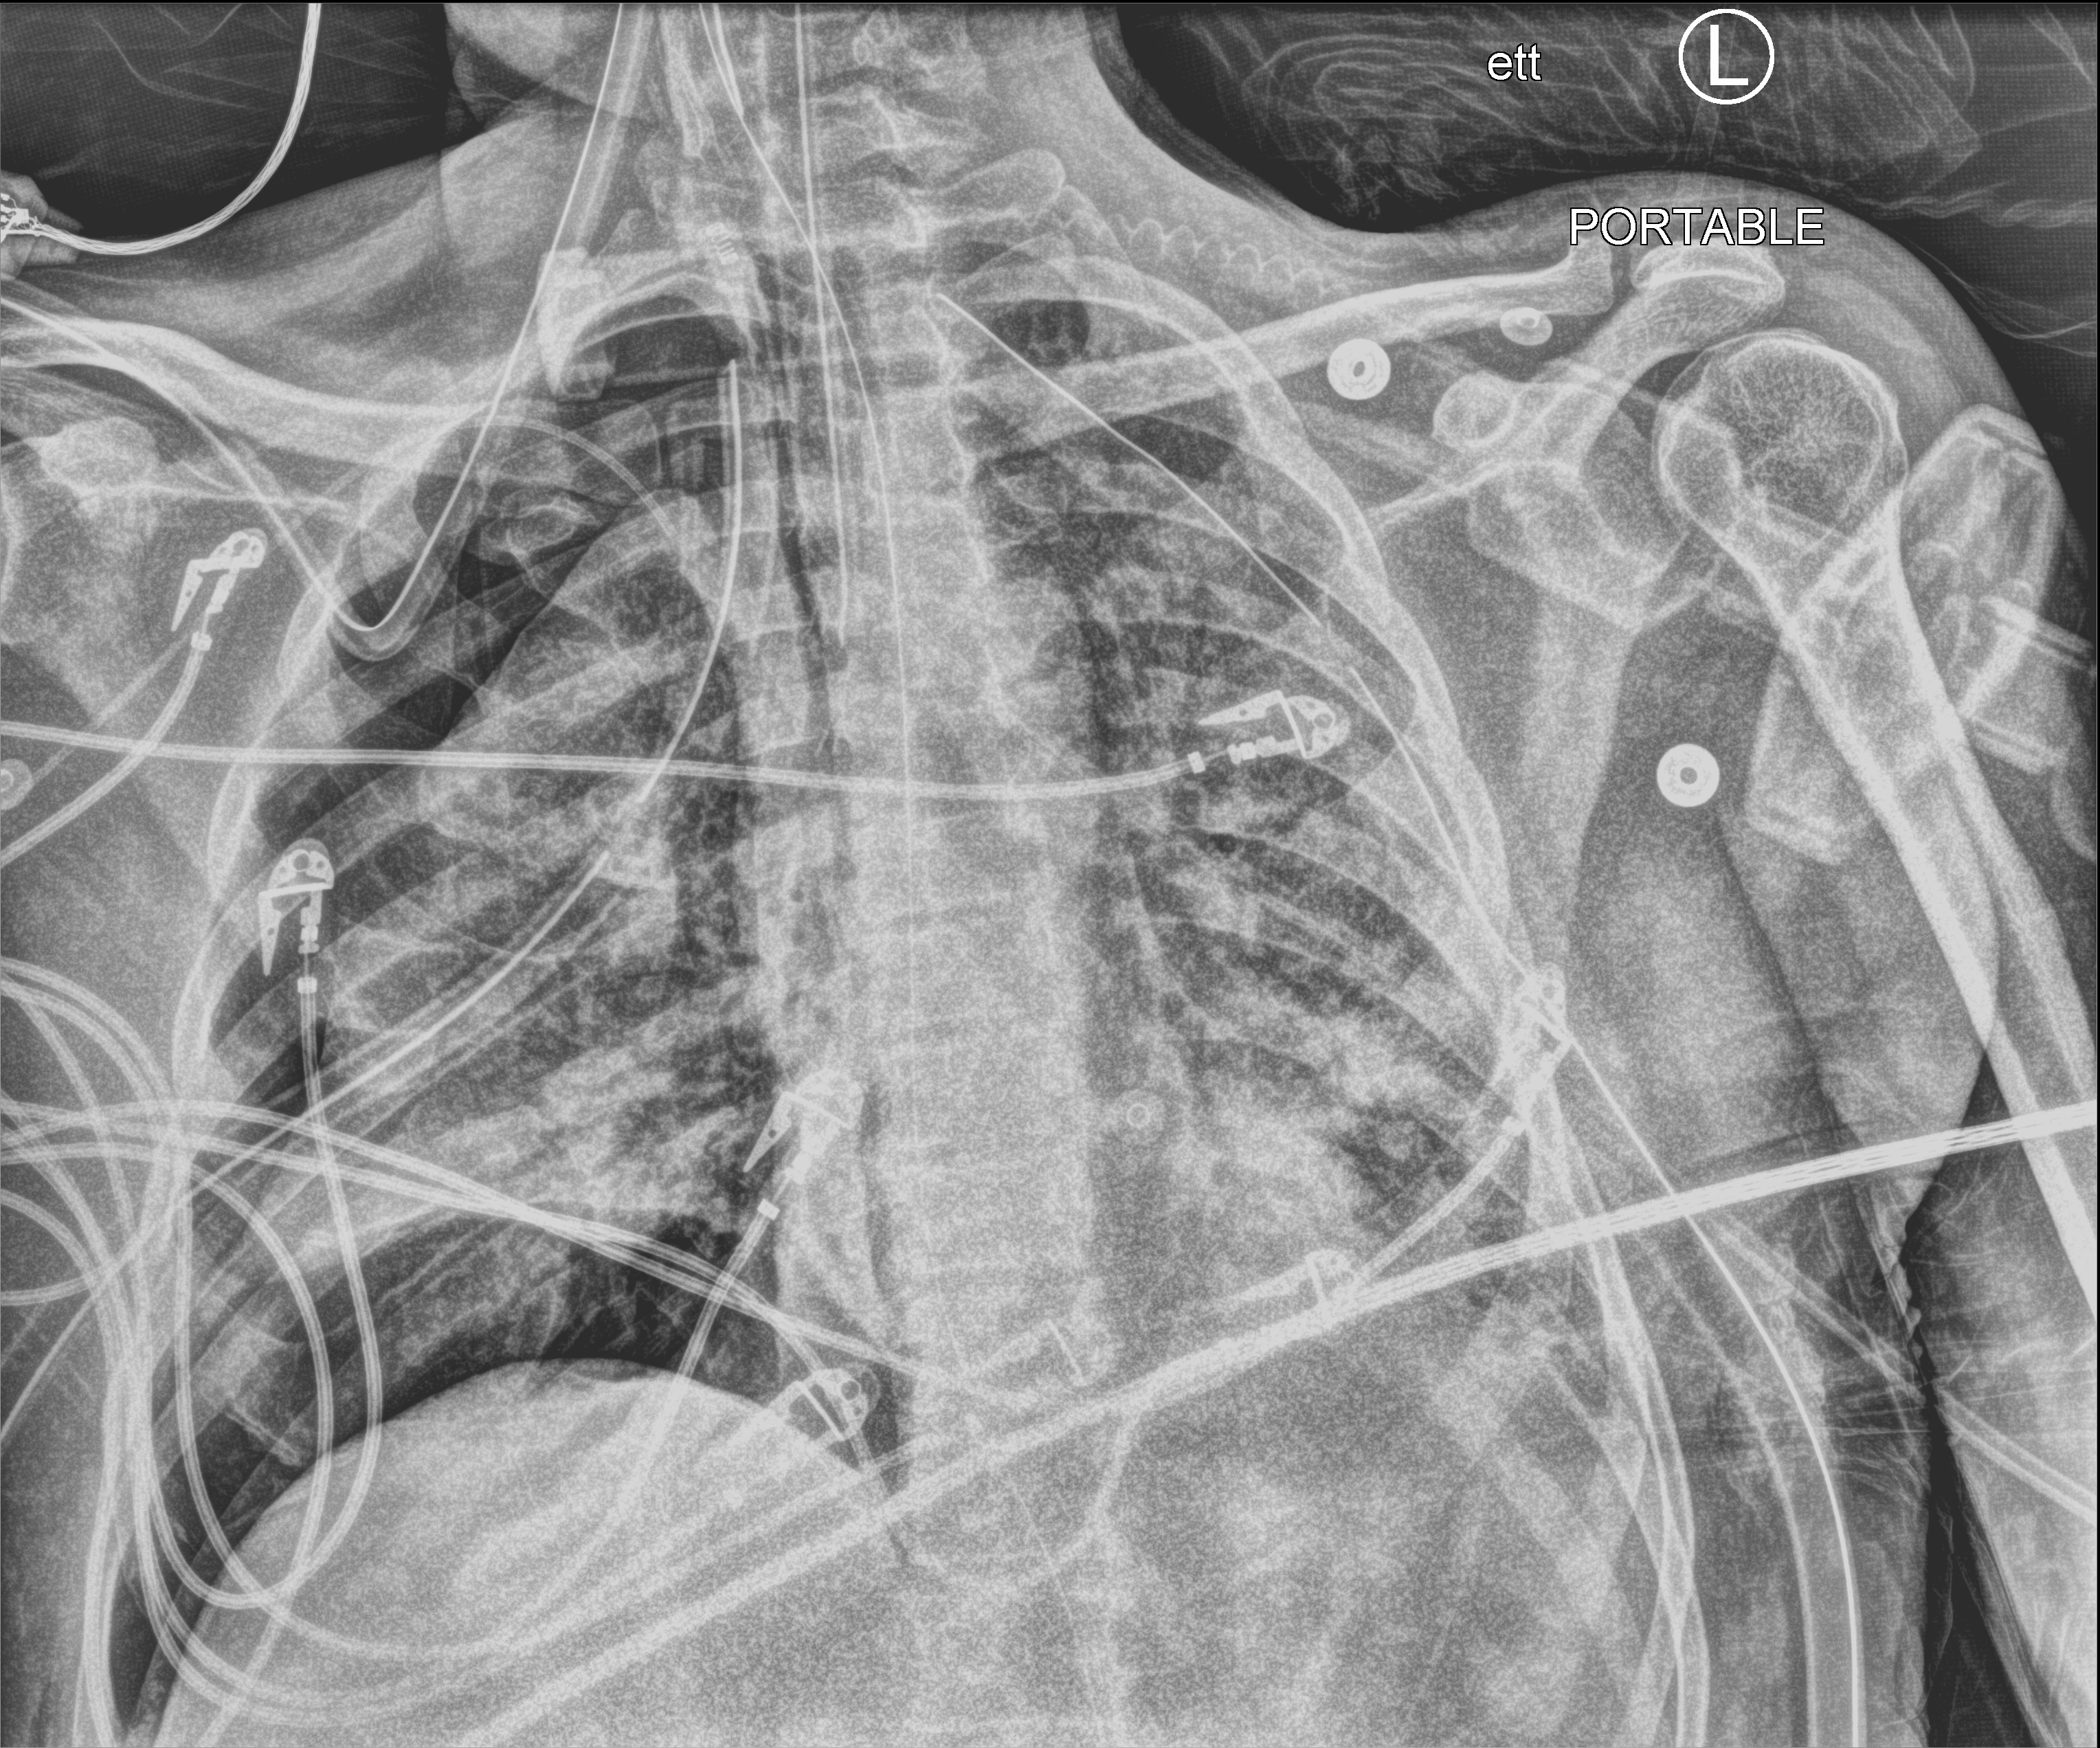
Bedside chest radiograph (computed radiography), anteroposterior (AP) projection. Patient hospitalised with COVID-19; male, aged 18–59 years.
From the hospital-stay record, not from the radiograph (when in the stay this image was taken is not recorded):
- mechanically ventilated during this hospital stay: yes
- smoking status (admission record): never